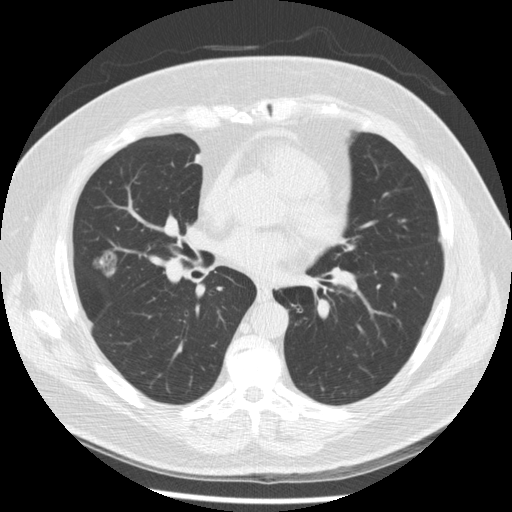
Low-dose screening chest CT, one axial slice. Slice 113 of 230 in the series (ordered by position). Reconstruction kernel STANDARD. 120 kVp. Lung window (W 1500 / L -600 HU). 512 × 512 image matrix, field of view 360 × 360 mm.
Structures marked on this image (manually delineated by an expert):
- lesion 1 (tumor, middle lobe of right lung): bounding box (x1, y1, x2, y2) in pixels: (95, 252, 118, 278)